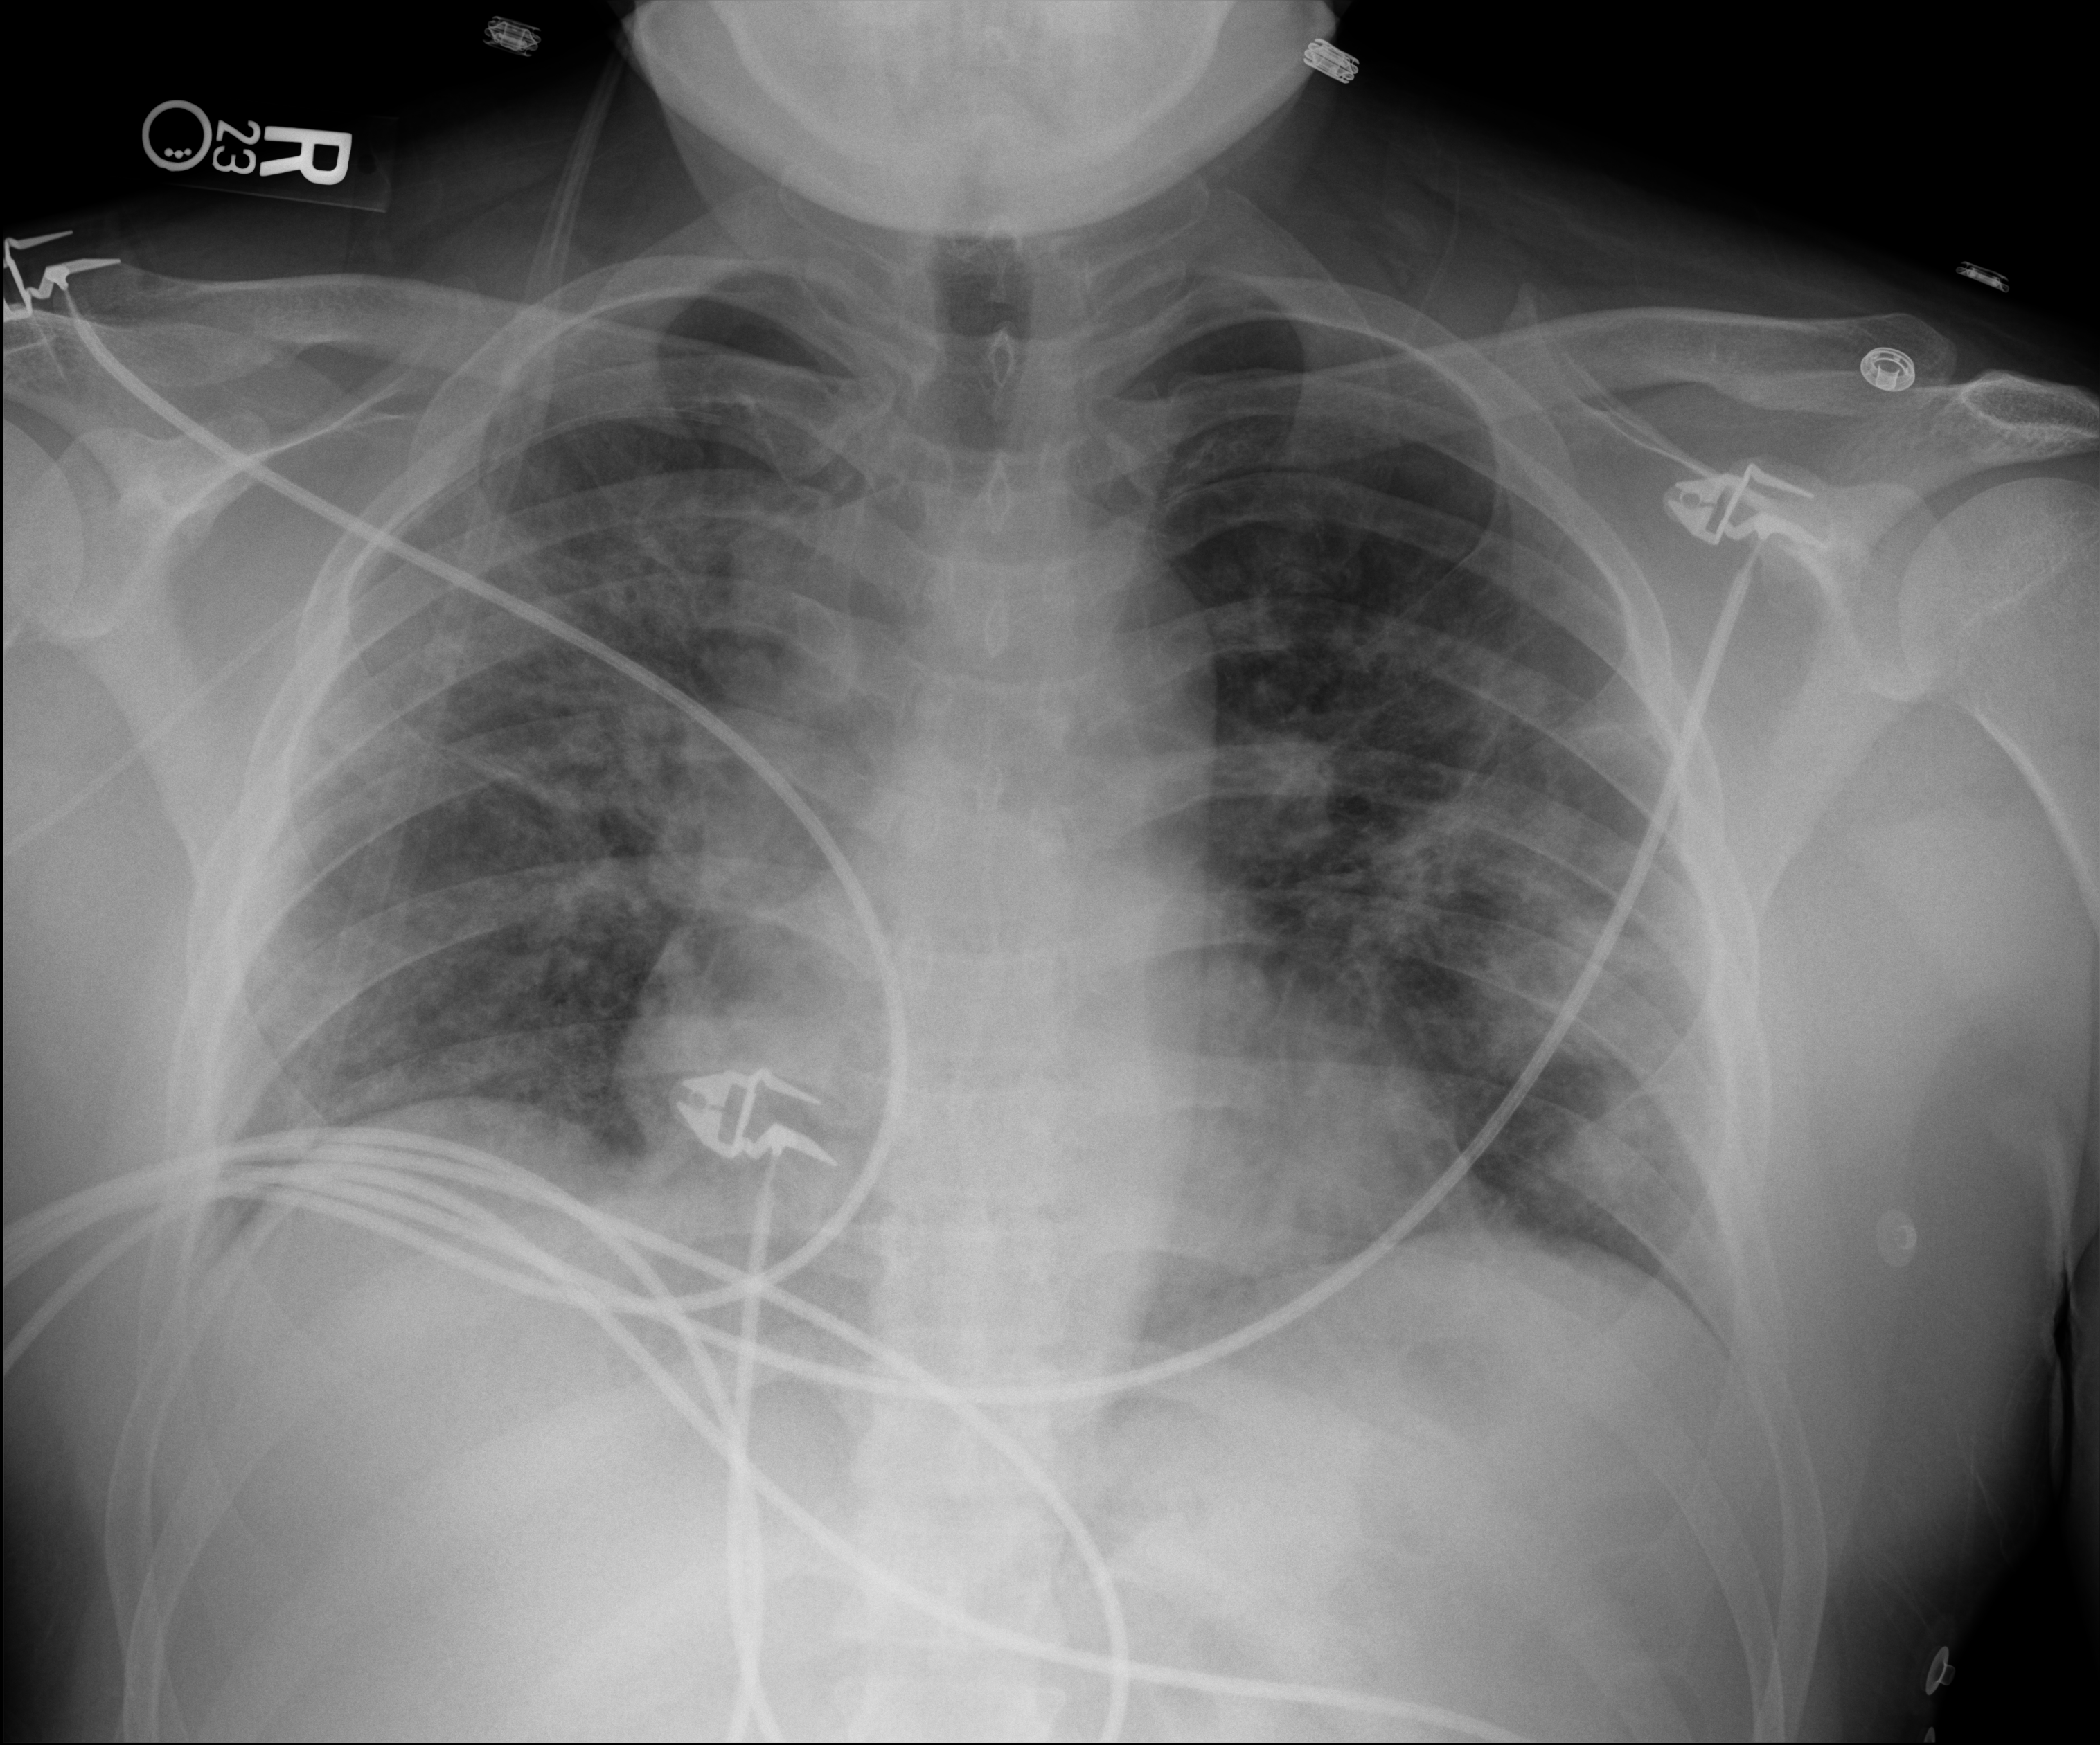
Portable chest radiograph; anteroposterior (AP) projection. Patient hospitalised with COVID-19; male, aged 18–59 years.
From the hospital-stay record, not from the radiograph (when in the stay this image was taken is not recorded): mechanically ventilated during this hospital stay: no; admitted to intensive care during this hospital stay: no; COPD (admission record): no.